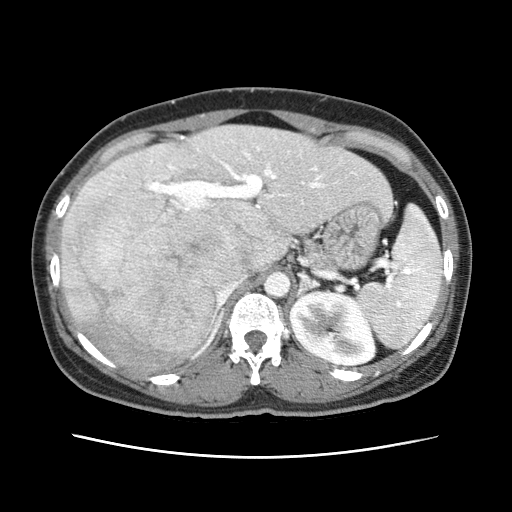
Contrast-enhanced abdominal CT (liver protocol), one axial slice. Slice 39 of 79 in the series (ordered by position). Soft-tissue window (W 400 / L 40 HU). 512 × 512 image matrix, field of view 340 × 340 mm. Case-level facts recorded for this patient, not image findings: diagnosis: hepatocellular carcinoma (patient treated with transarterial chemoembolisation; whether this scan precedes or follows treatment is not stated here); TNM stage (as recorded): Stage-I; Child-Pugh class: A; tumour nodularity: uninodular.
Annotated regions visible in this slice (semi-automatic segmentation, software-assisted and operator-edited):
- abdominal aorta: bounding box [x1, y1, x2, y2] px = [264, 271, 290, 297]
- liver parenchyma outside the tumour (the mass and vessels are separate outlines, so this box may not span the whole liver): [60, 125, 390, 372]
- mass: [68, 187, 257, 364]
- liver vessels: [91, 147, 353, 332]